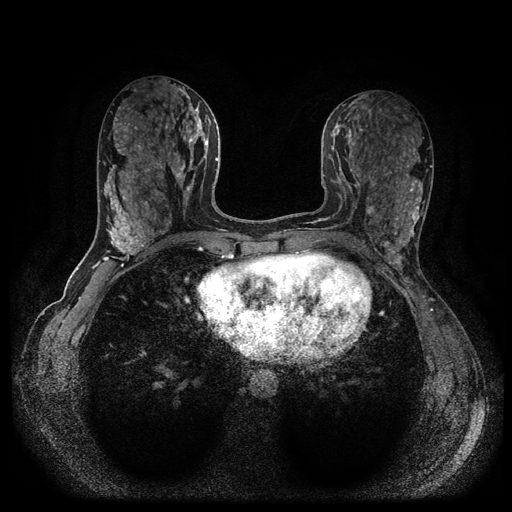
Breast MRI (dynamic contrast-enhanced, multi-phase), one axial slice; slice 45 of 116 in the series (ordered by position); dynamic contrast-enhanced series, time point 2 of 5 at this slice position (early post-contrast); 1.5 T; TE 2.6 ms, TR 5.4 ms; 512 × 512 image matrix. Patient: female, 43 years.
Structures marked on this image (semi-automatic segmentation, software-assisted and operator-edited):
- breast lesion (labelled benign in the annotation): bounding box (x1, y1, x2, y2) in pixels: (366, 201, 379, 218)